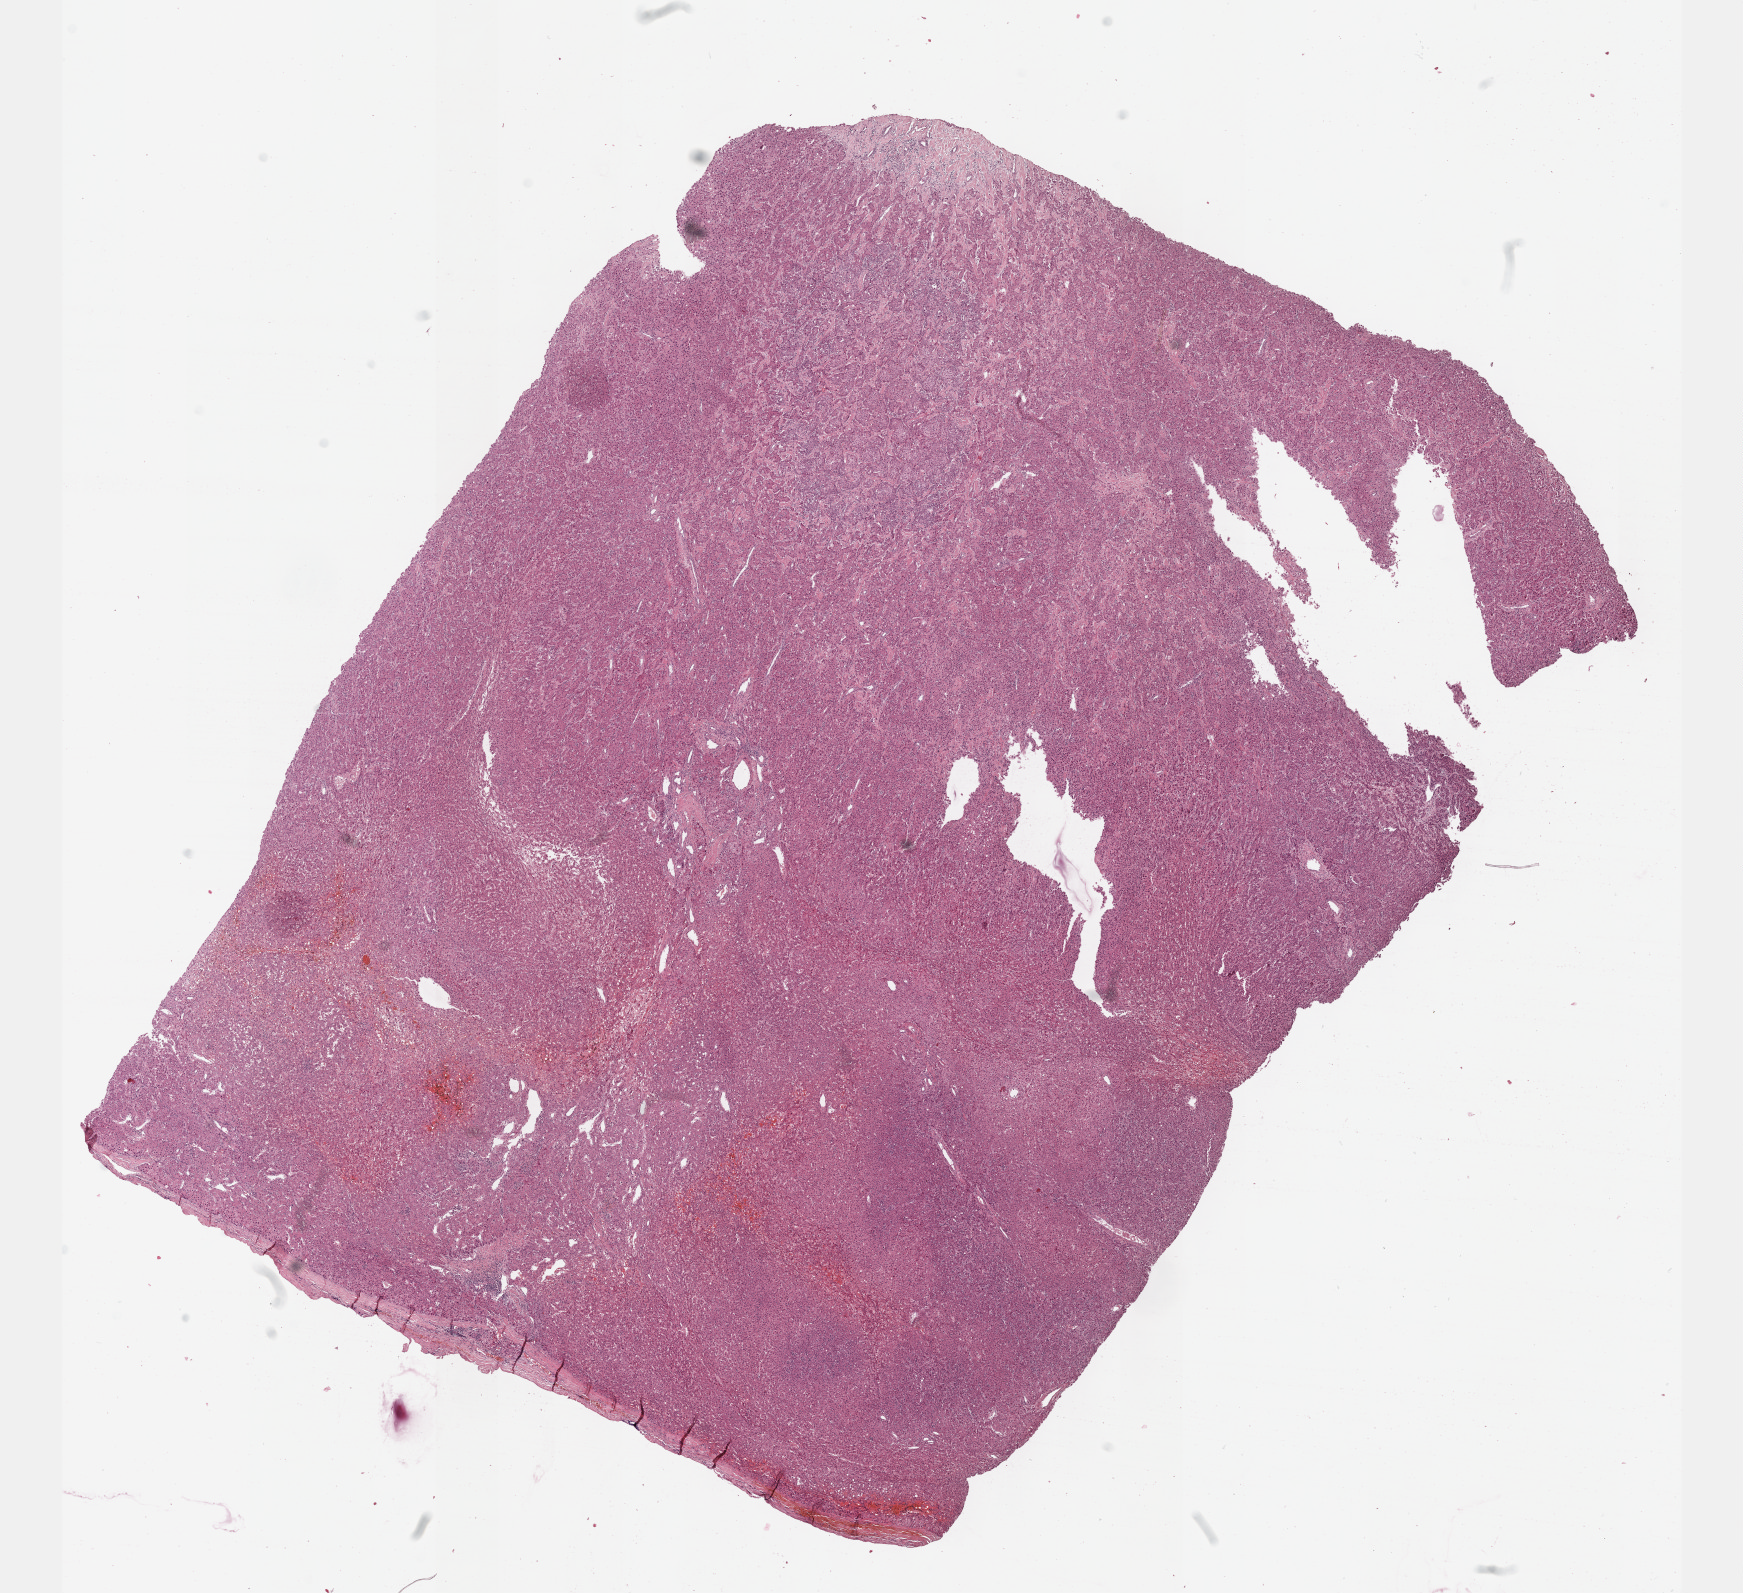
Digitized H&E-stained tissue section (whole slide) — a low-resolution overview of the entire scanned area, about 14.1 x 12.9 mm. Formalin-fixed paraffin-embedded (FFPE) diagnostic section. Liver, primary tumour sample. Female, age 65 years at initial diagnosis. Histologic grade: G2 (moderately differentiated).
- pathologic diagnosis: Hepatocellular carcinoma, NOS
- AJCC pathologic stage: II
- TNM: T2 N0 M0